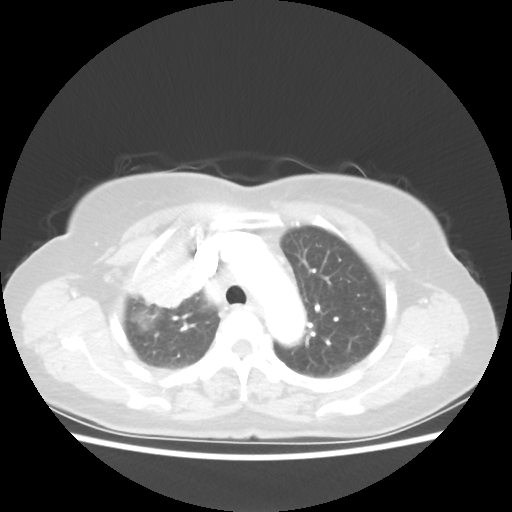
Chest CT, one axial slice. Position 40 of 55 along the scan axis. Reconstruction kernel STANDARD. 80 kVp. Lung window (W 1500 / L -600 HU). 5 mm slice thickness. 512 × 512 image matrix, field of view 337 × 337 mm. Female patient, age 62 years. Case-level facts recorded for this patient, not image findings: clinical TNM (as recorded): T4 N3 M0.
Annotated regions visible in this slice (rectangle marked by the reading radiologist):
- lung tumour (recorded histology: squamous cell carcinoma): bounding box (x1, y1, x2, y2) in pixels: (123, 241, 204, 310)